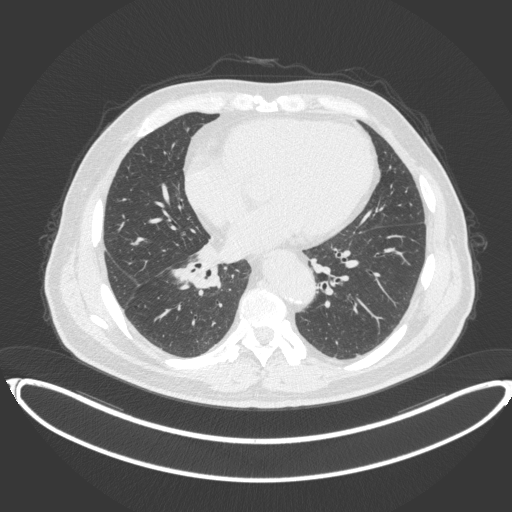
Chest CT, one axial slice; position 169 of 383 along the scan axis; reconstruction kernel B31f; 120 kVp; lung window (W 1500 / L -600 HU); 1 mm slice thickness; 512 × 512 image matrix. Patient: male, 61 years. Case-level facts recorded for this patient, not image findings: clinical TNM (as recorded): T1b N1 M0.
Outlined on this slice (rectangle marked by the reading radiologist):
- lung tumour (recorded histology: squamous cell carcinoma): bounding box <179,262,221,293> (left, top, right, bottom; pixels)